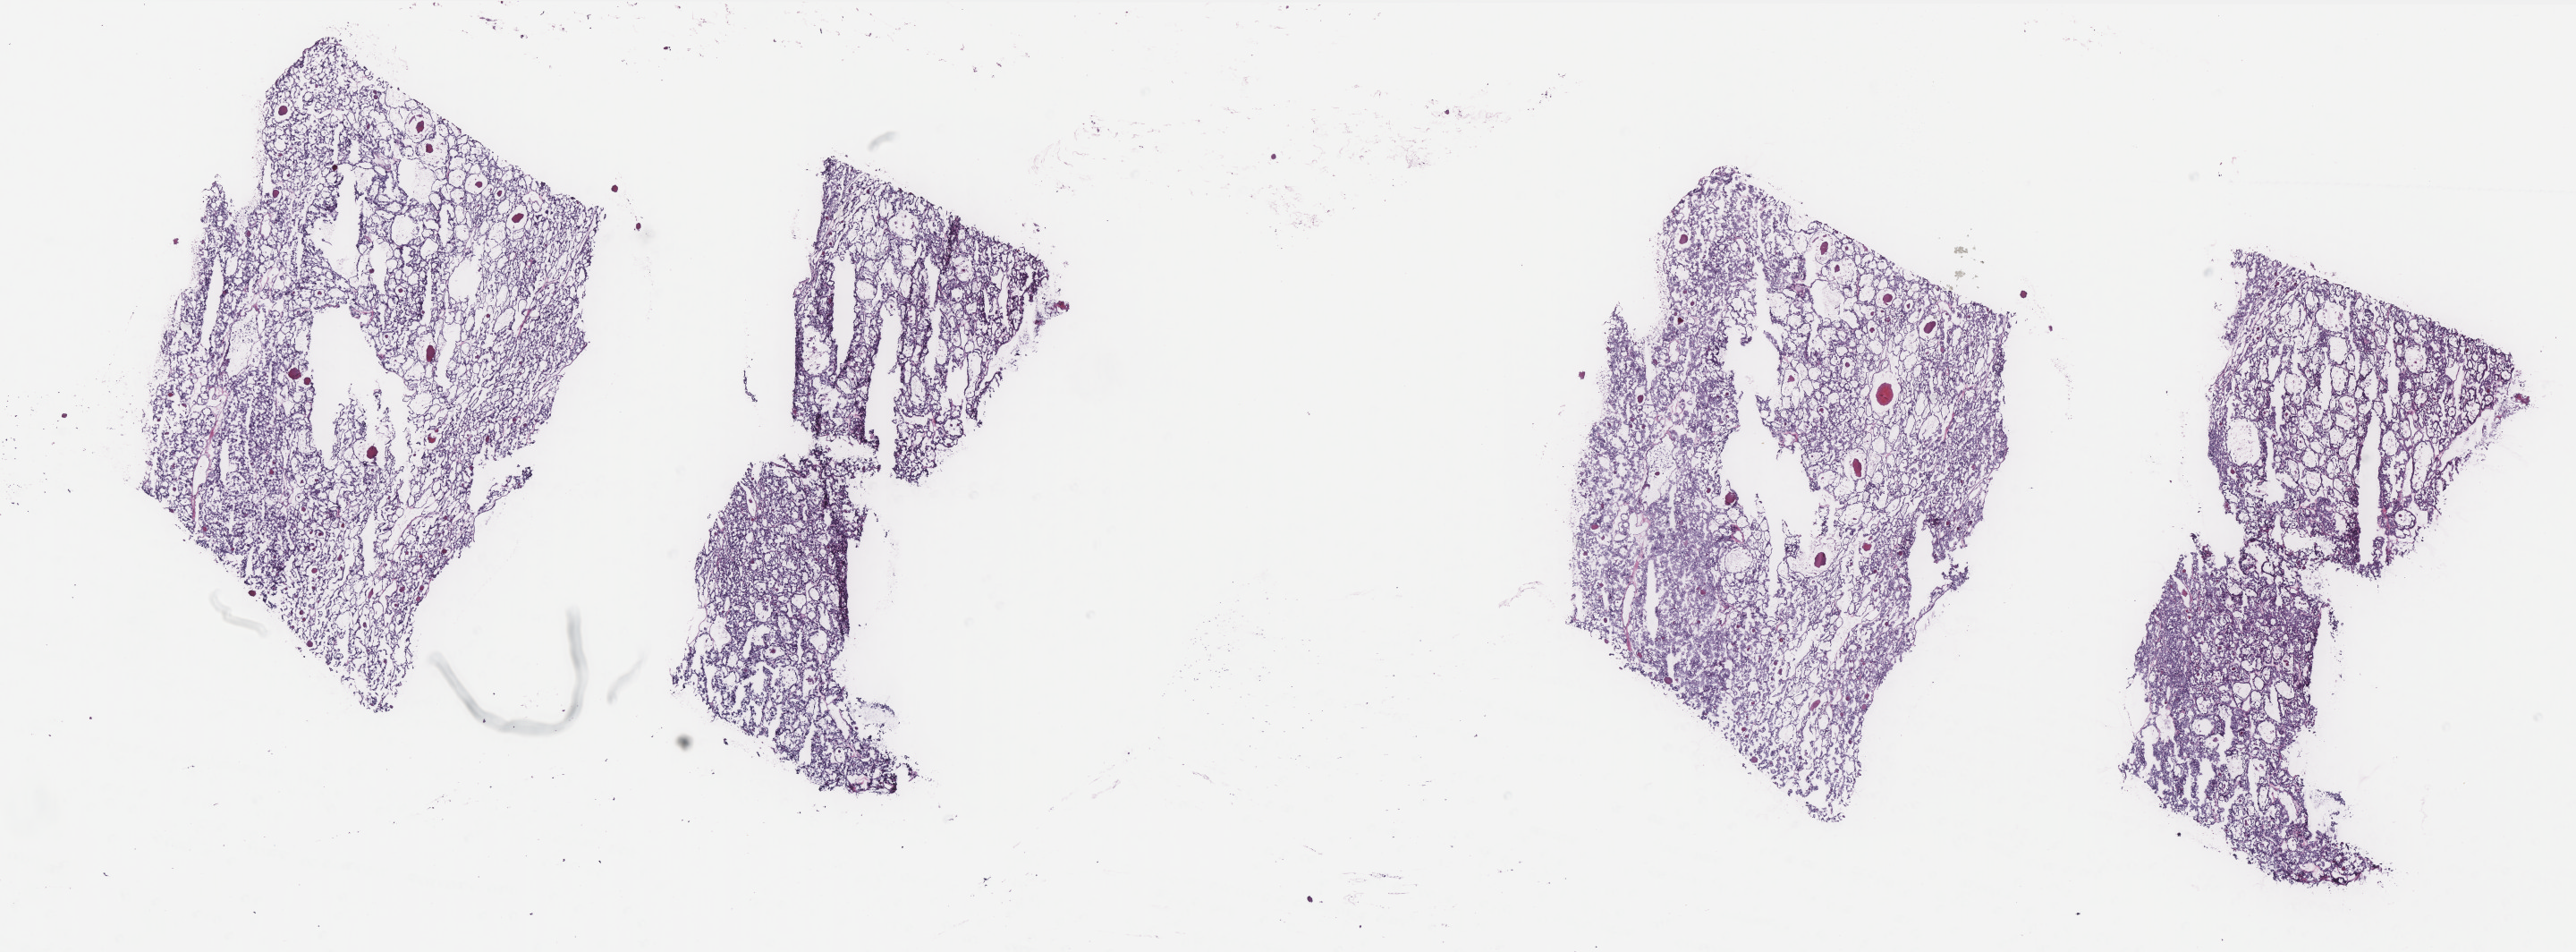
Hematoxylin and eosin (H&E) stained whole-slide image — whole scanned area (about 23.1 x 8.5 mm, acquisition: 40x scan) shown as a low-resolution overview. Frozen section. Sample: primary tumour, thyroid. Patient: female, age at initial diagnosis 63 years. Slide review estimates, as recorded: tumour cells 100%, tumour nuclei 95%.
Pathologic diagnosis: Papillary adenocarcinoma, NOS (thyroid gland).